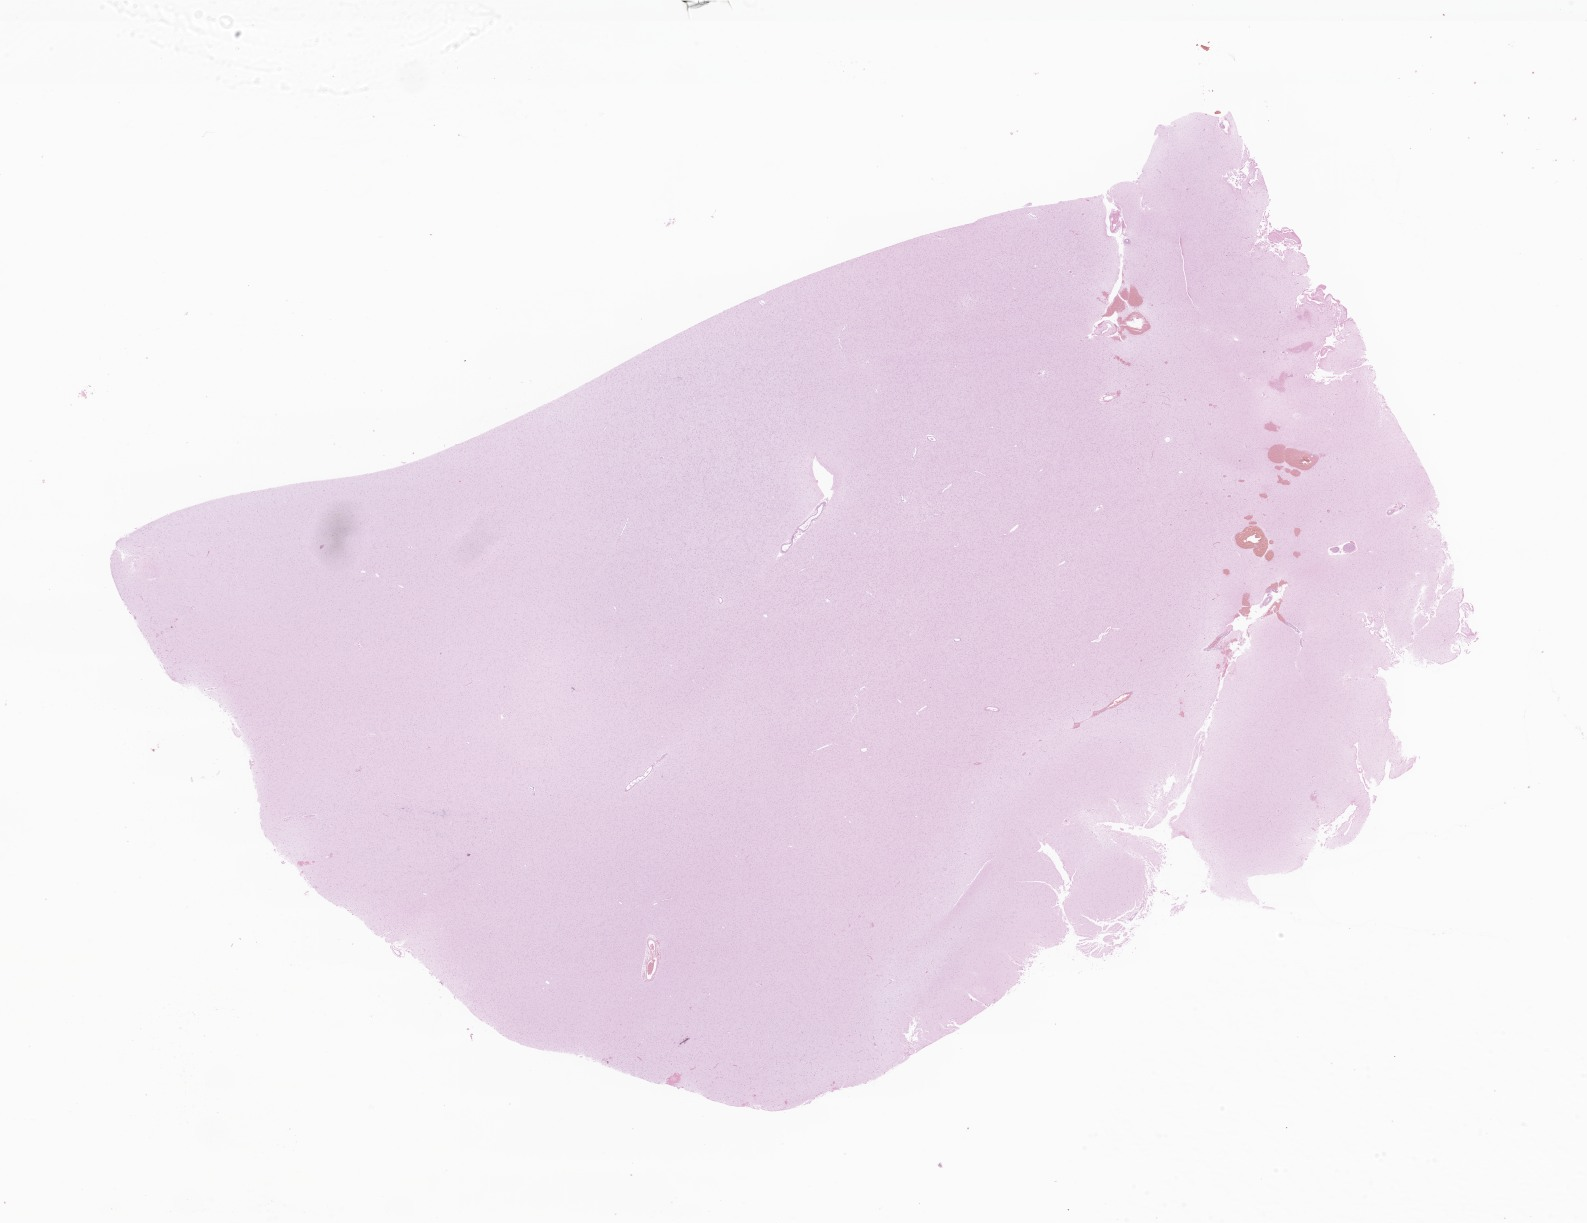
Digitized haematoxylin and eosin-stained section of tumor tissue from the temporal lobe — low-resolution overview of the scanned area, about 26.8 x 20.6 mm. FFPE section. Patient: female, age 81 months (6 years 9 months).
Recorded diagnosis: Glioma, malignant.